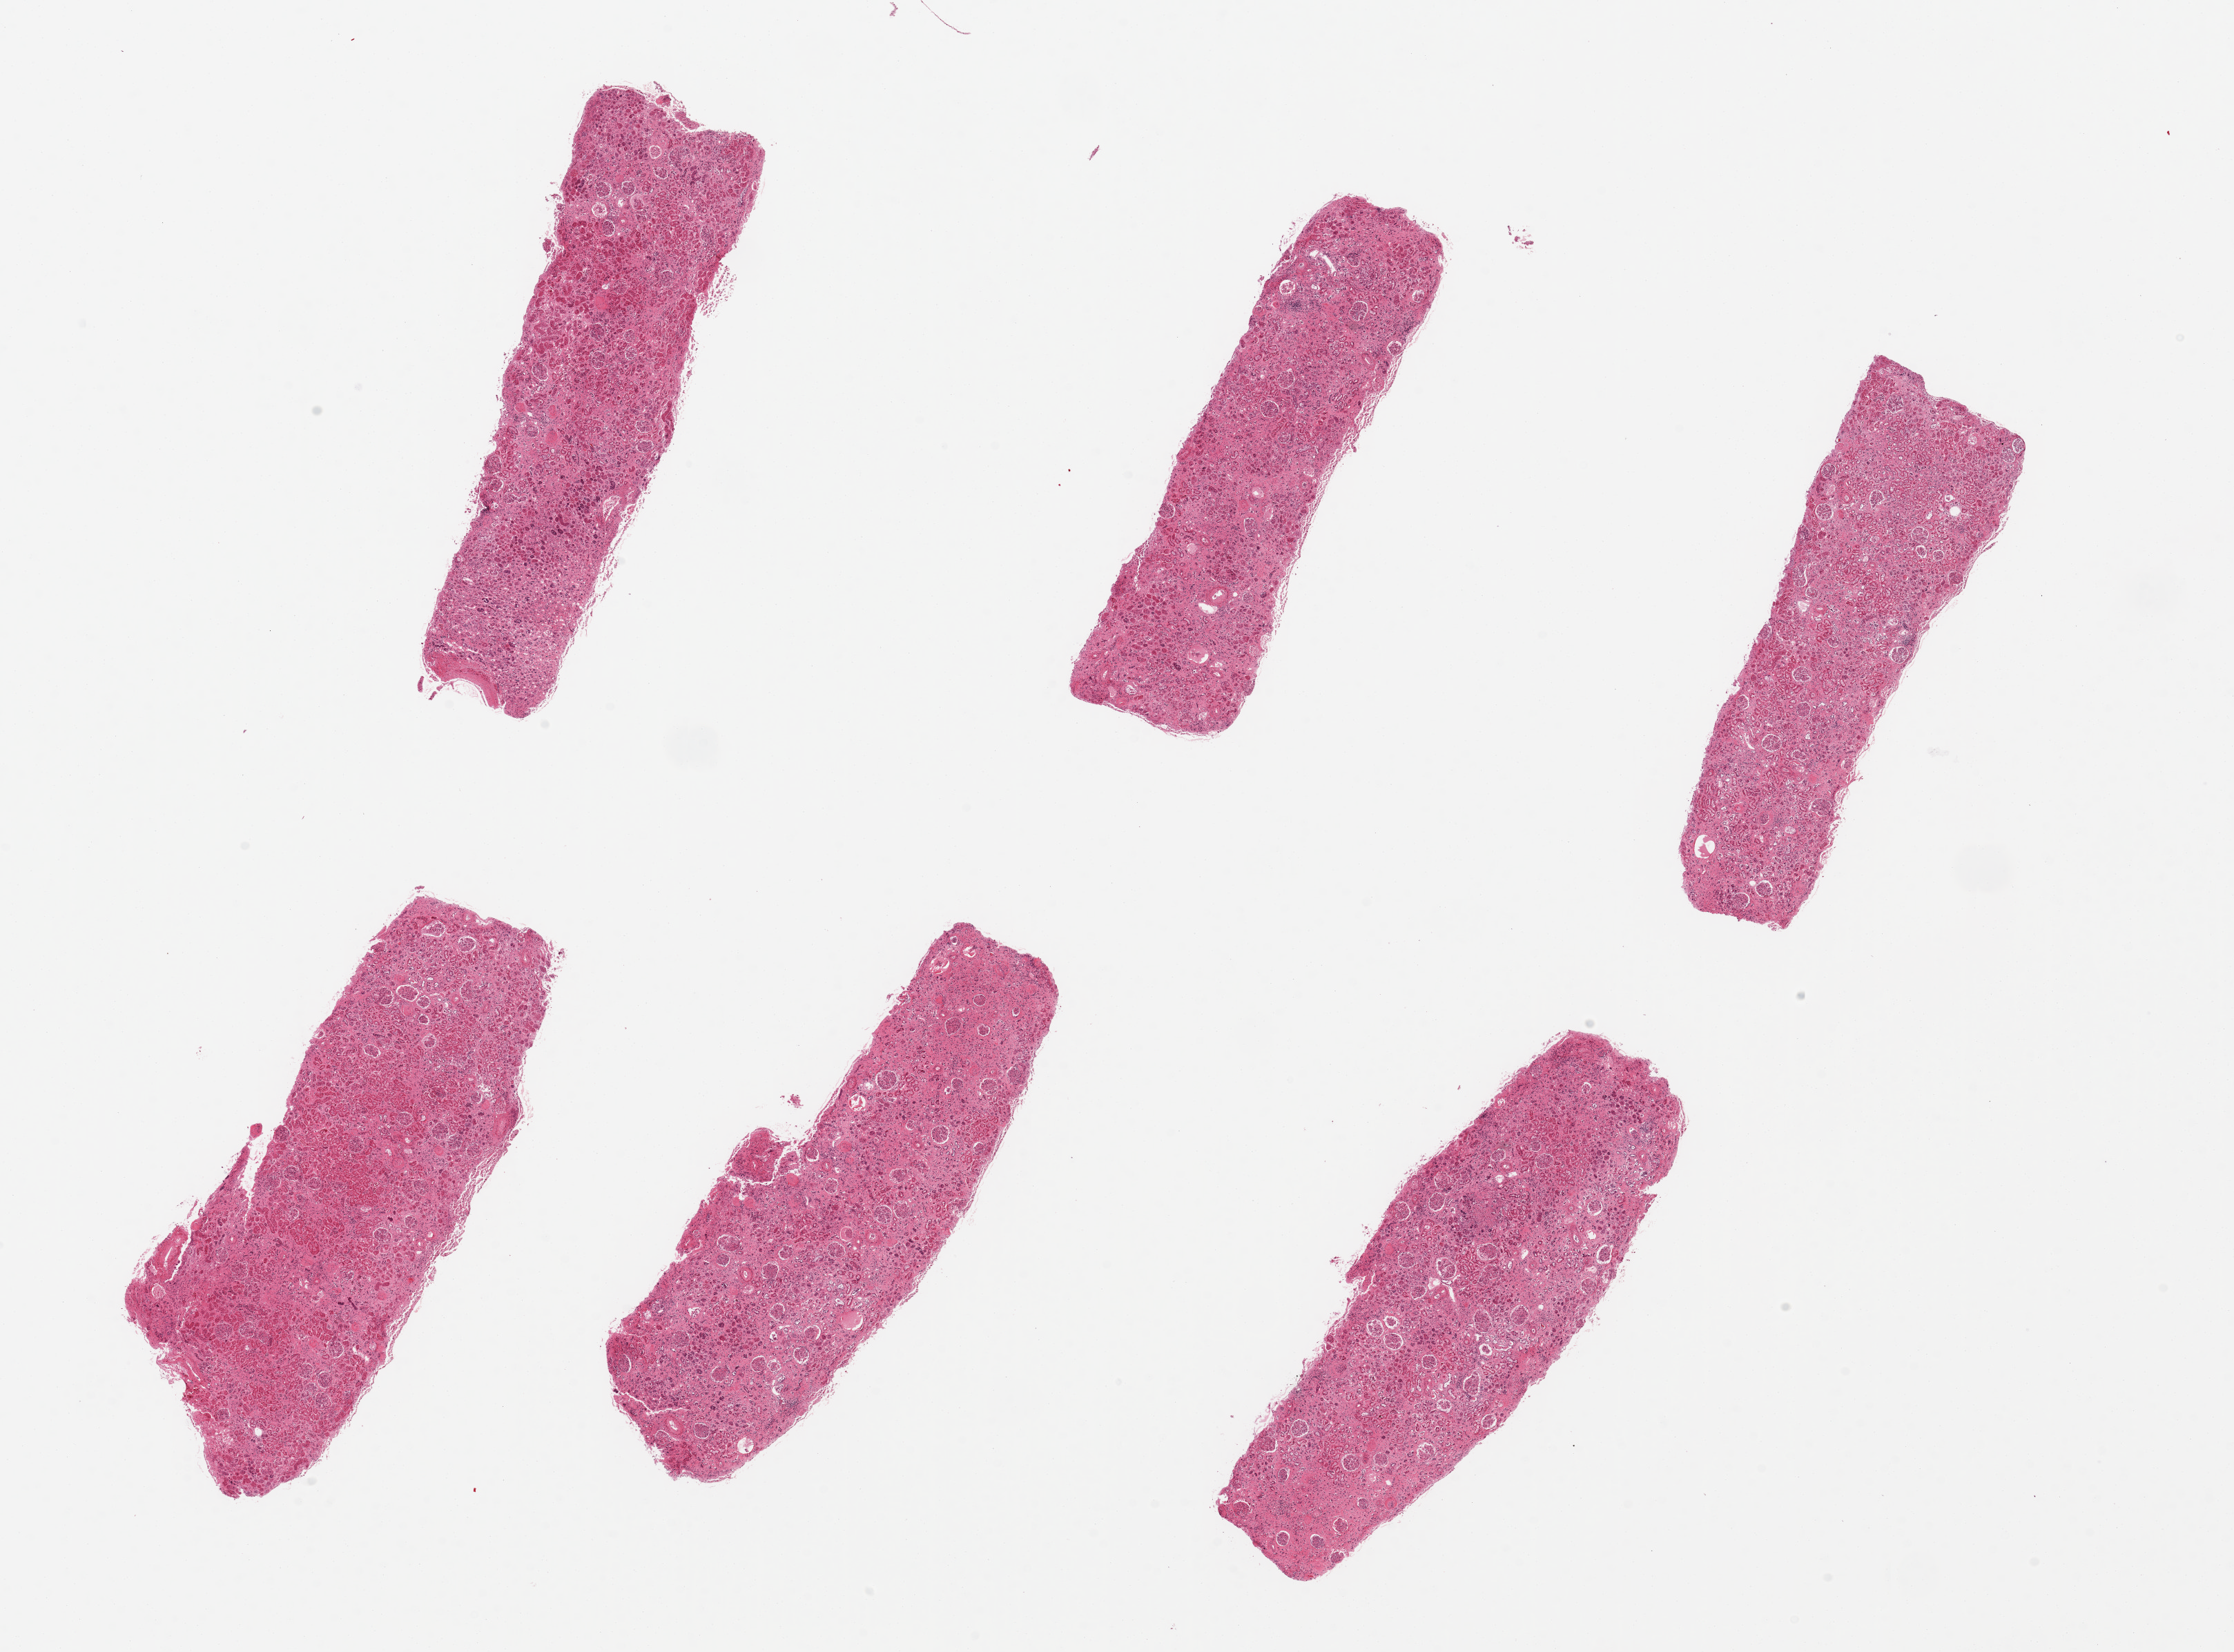
Haematoxylin and eosin whole-slide image, low-resolution overview of the scanned area, about 25.6 x 18.9 mm. PAXgene-fixed, paraffin-embedded tissue. Sampled site (target tissue): renal cortex. Tissue donor sample. Donor sex: male.
Pathologist's review note for this sample: 6 pieces up to 7x3 mm; marked arterial and arteriolar sclerosis; tubules autolyzed; moderate interstitial fibrosis; virtually all cortex.